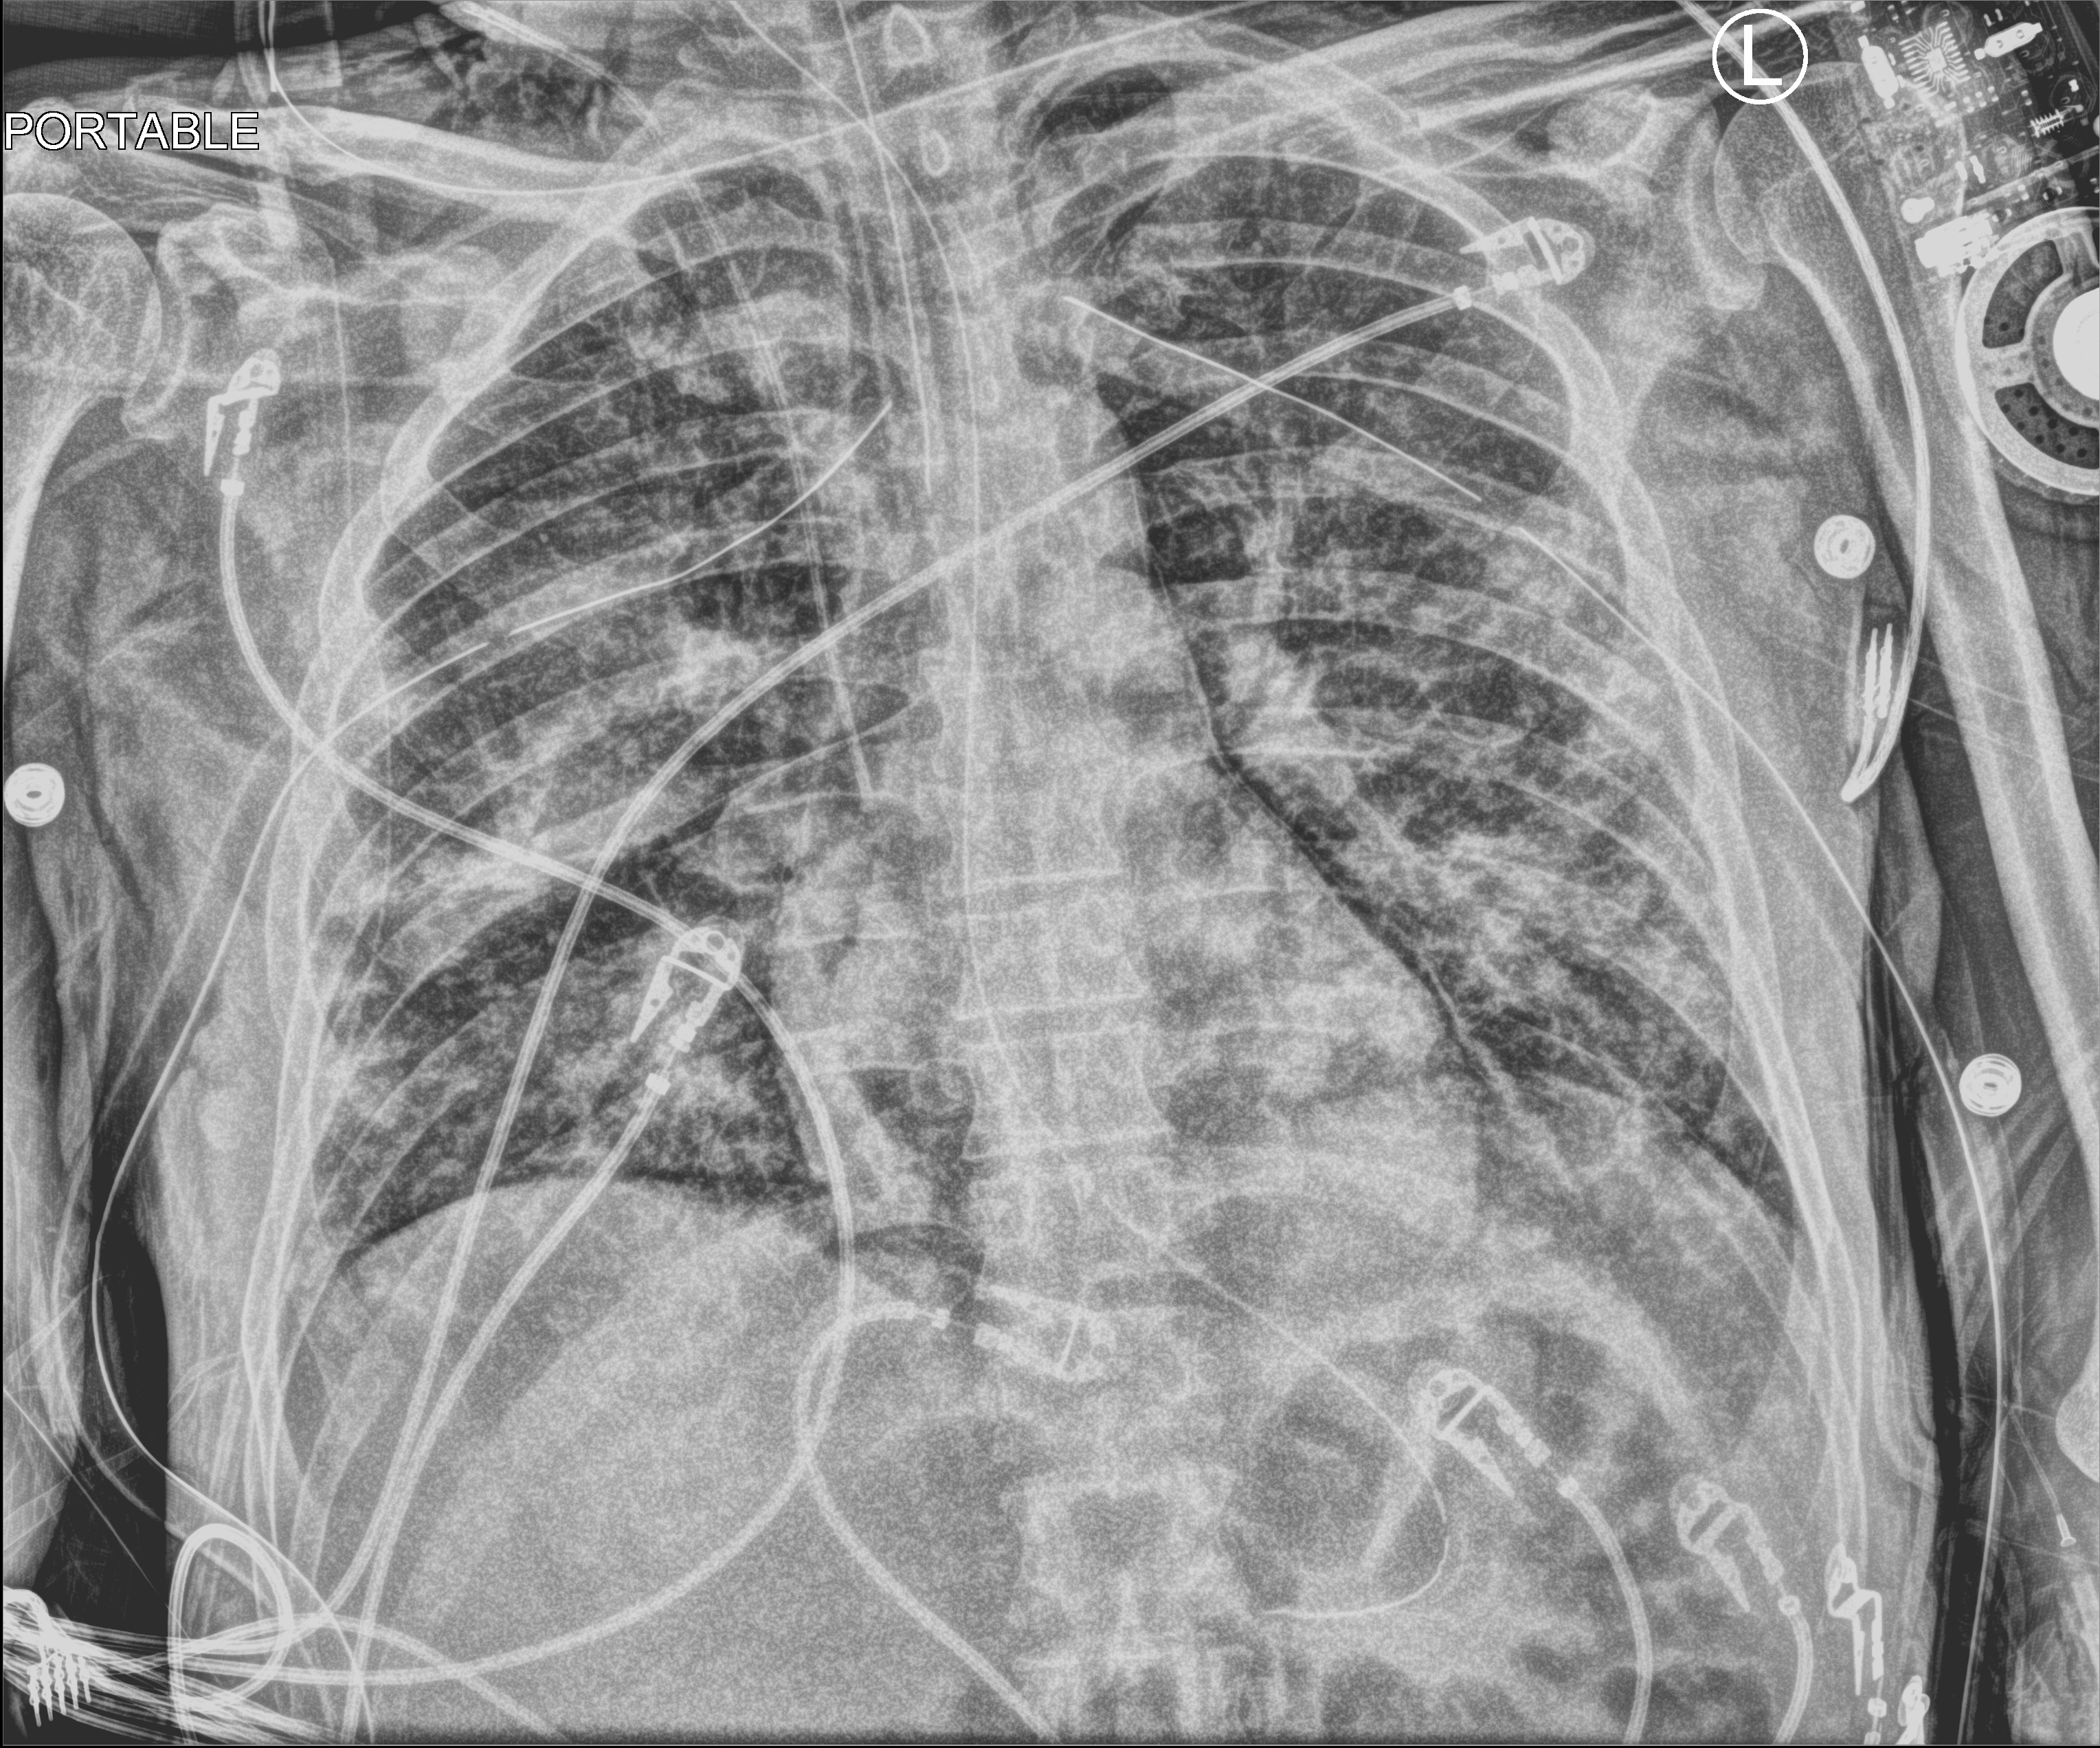
Portable chest radiograph; anteroposterior (AP) projection. Patient hospitalised with COVID-19; male, aged 18–59 years.
Admission-level facts for this patient (not findings on this image; timing relative to this image not recorded): hypertension (admission record): yes.